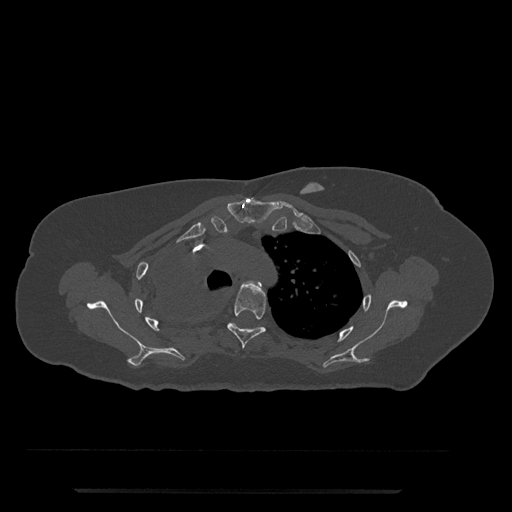
CT including the spine, one axial slice. Slice 588 of 797 in the series (ordered by position). Reconstruction kernel Br40s/3. 120 kVp. Bone window (W 1800 / L 400 HU). 512 × 512 image matrix, field of view 440 × 440 mm. Female patient, age 51 years. From the clinical record (not read from this slice): primary cancer: neuro.
Outlined on this slice (semi-automatic segmentation, software-assisted and operator-edited):
- T3 vertebra: bounding box <242,280,262,289> (left, top, right, bottom; pixels)
- T4 vertebra: <227,284,266,349>
- T5 vertebra: <231,323,261,330>